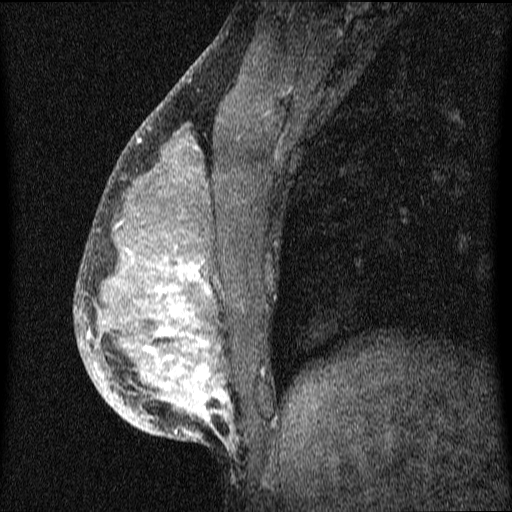
Breast MRI (dynamic contrast-enhanced), one sagittal slice. Slice 26 of 64 in the series (ordered by position). Dynamic contrast-enhanced series, image 2 of 4 at this slice position (ordered by acquisition). 1.5 T. TE 4.2 ms, TR 9.1 ms. 512 × 512 image matrix, field of view 180 × 180 mm. Female patient, age 33 years.
Annotated regions visible in this slice (semi-automatic segmentation, software-assisted and operator-edited):
- analysis volume of interest (the breast-tissue region the enhancement analysis was run in; not a lesion): bounding box [x1, y1, x2, y2] px = [75, 151, 336, 458]
- tumour enhancement mask (voxels above the 70 % enhancement threshold inside the analysis volume of interest): [89, 222, 232, 436]